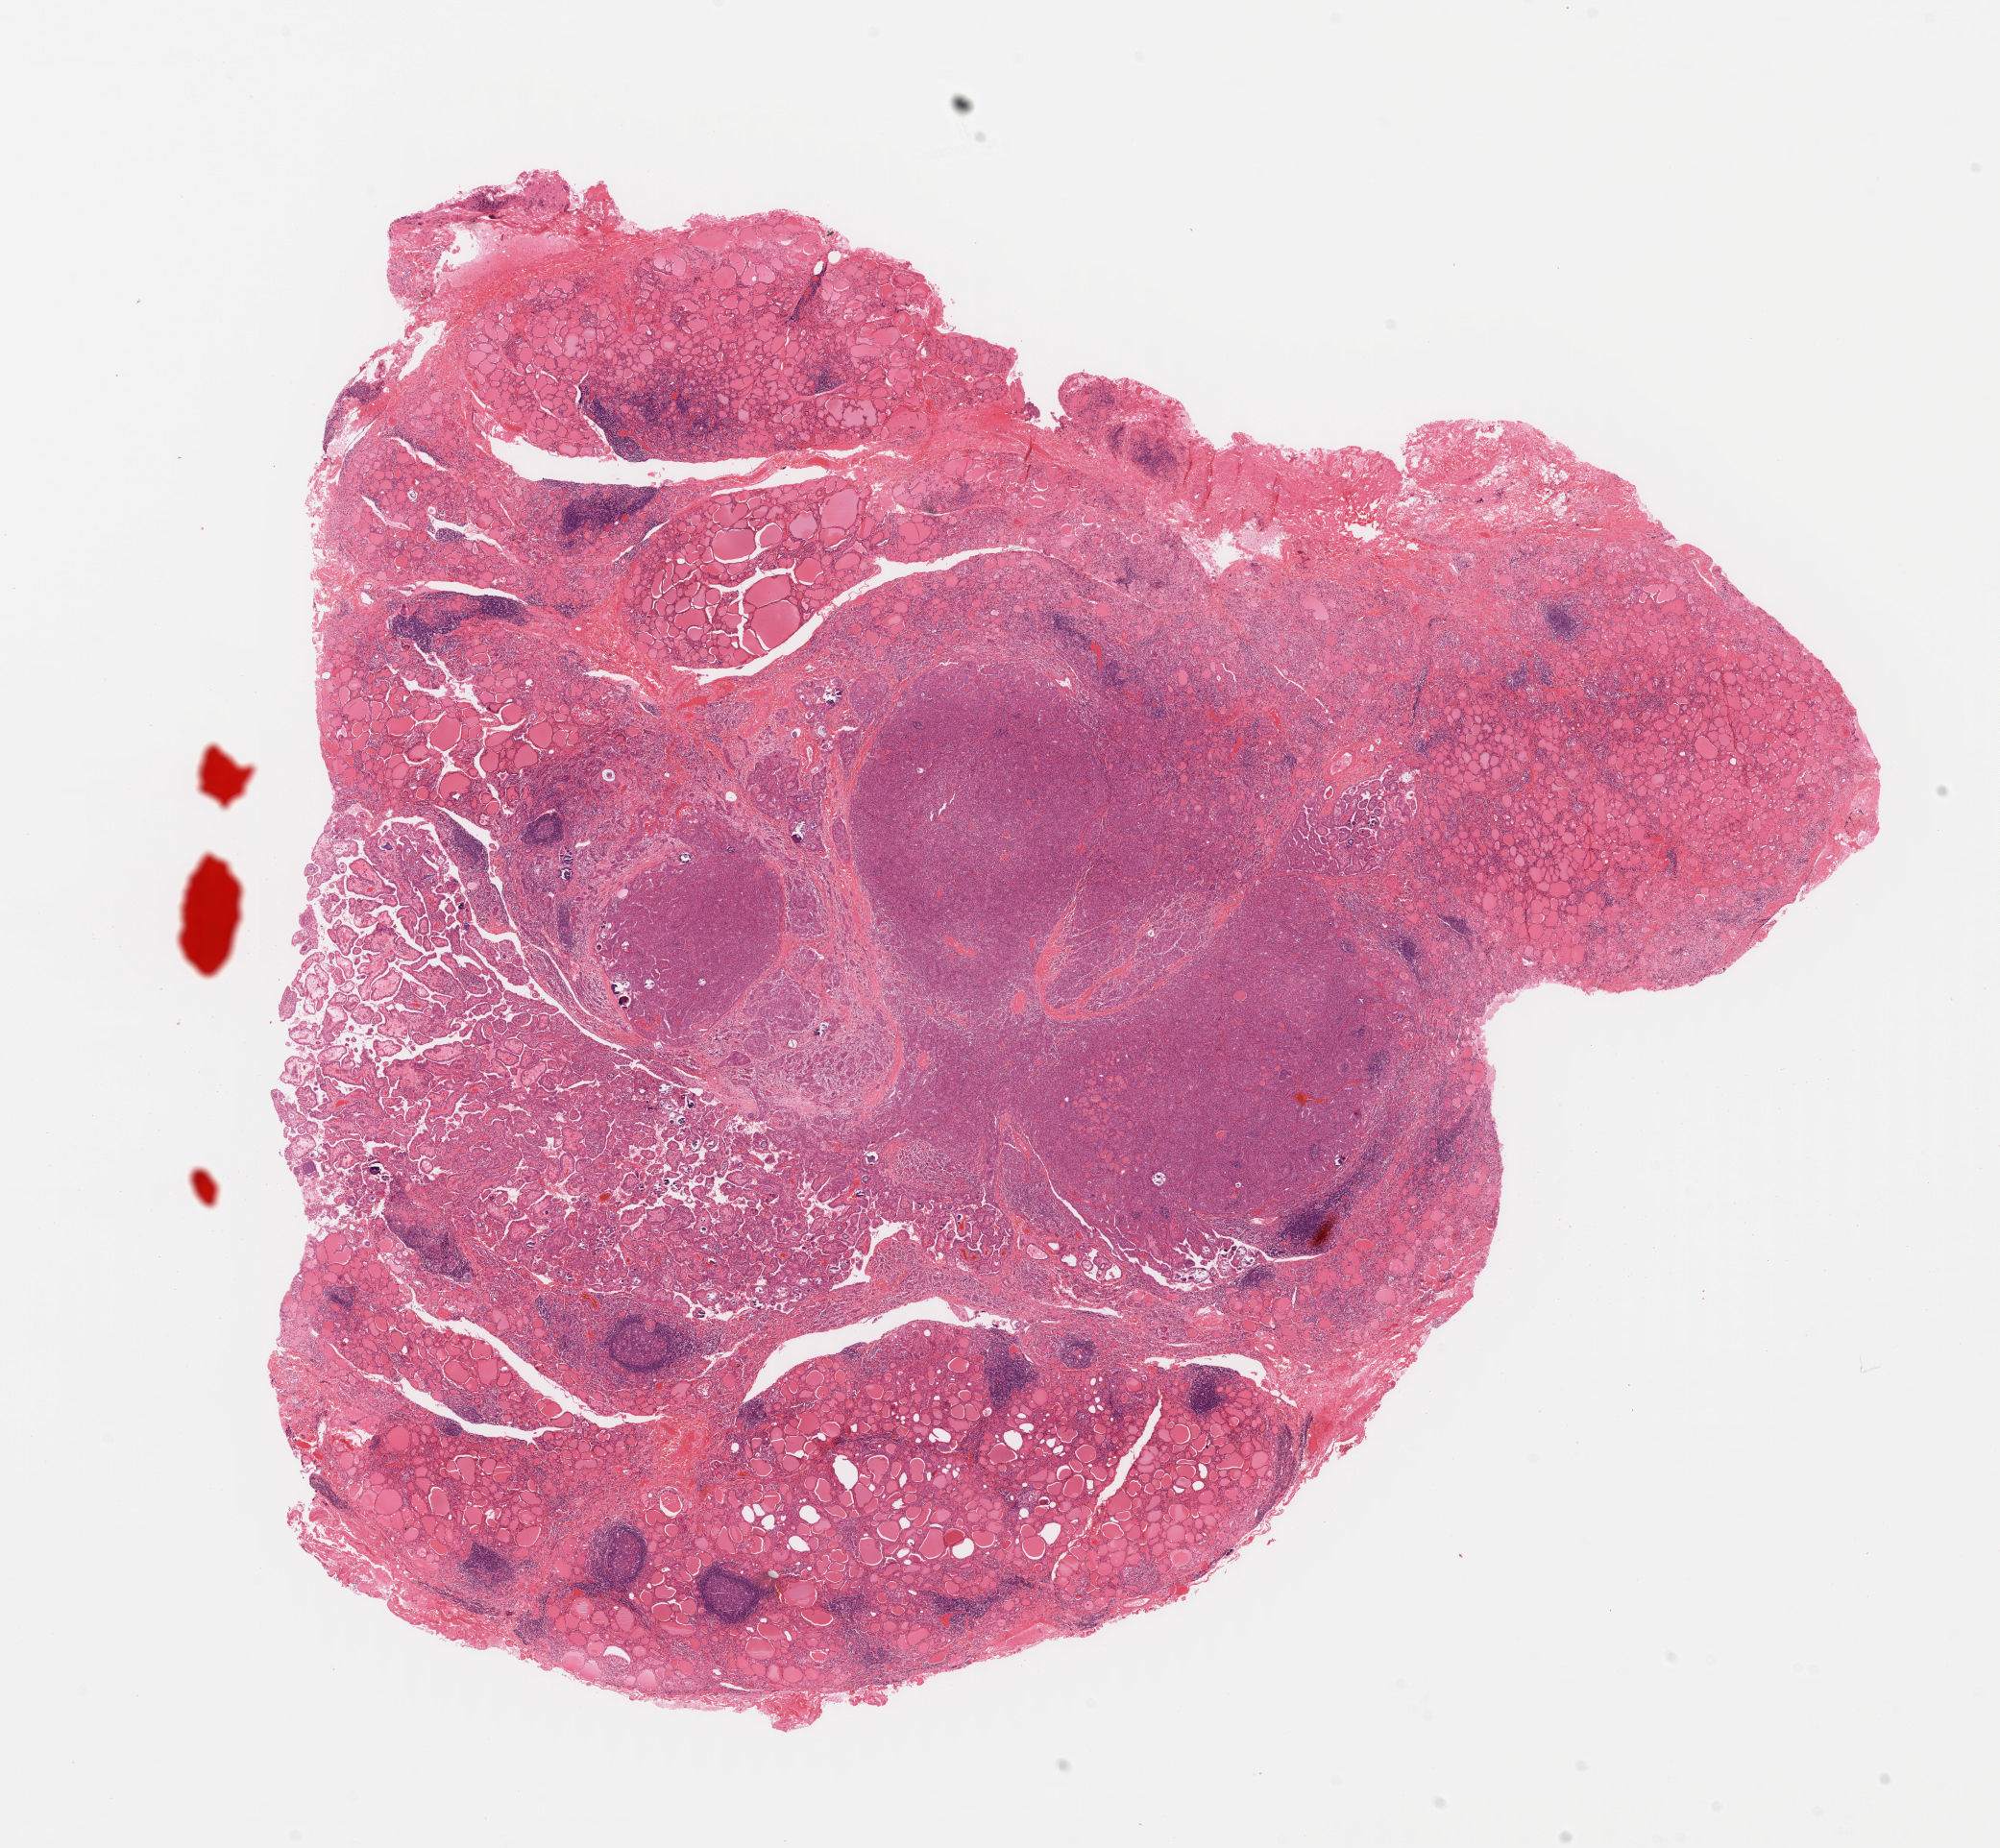
Whole-slide histology image, H&E-stained, whole scanned area (about 16.4 x 15.1 mm) shown as a low-resolution overview; formalin-fixed paraffin-embedded (FFPE) diagnostic section; sample: primary tumour, thyroid. Female patient; age at initial diagnosis 23 years.
Histologic diagnosis: Papillary adenocarcinoma, NOS (thyroid gland).